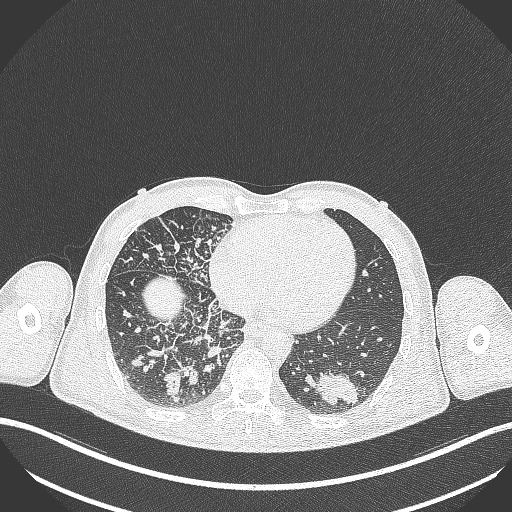
Chest CT, one axial slice; position 101 of 348 along the scan axis; reconstruction kernel B70f; lung window (W 1500 / L -600 HU); 512 × 512 image matrix. Patient: male, 49 years. From the clinical record (not read from this slice): clinical TNM (as recorded): T2b N1 M0.
Structures marked on this image (bounding box drawn by a radiologist):
- lung tumour (recorded histology: adenocarcinoma): box from (x=316, y=365) to (x=362, y=407) px